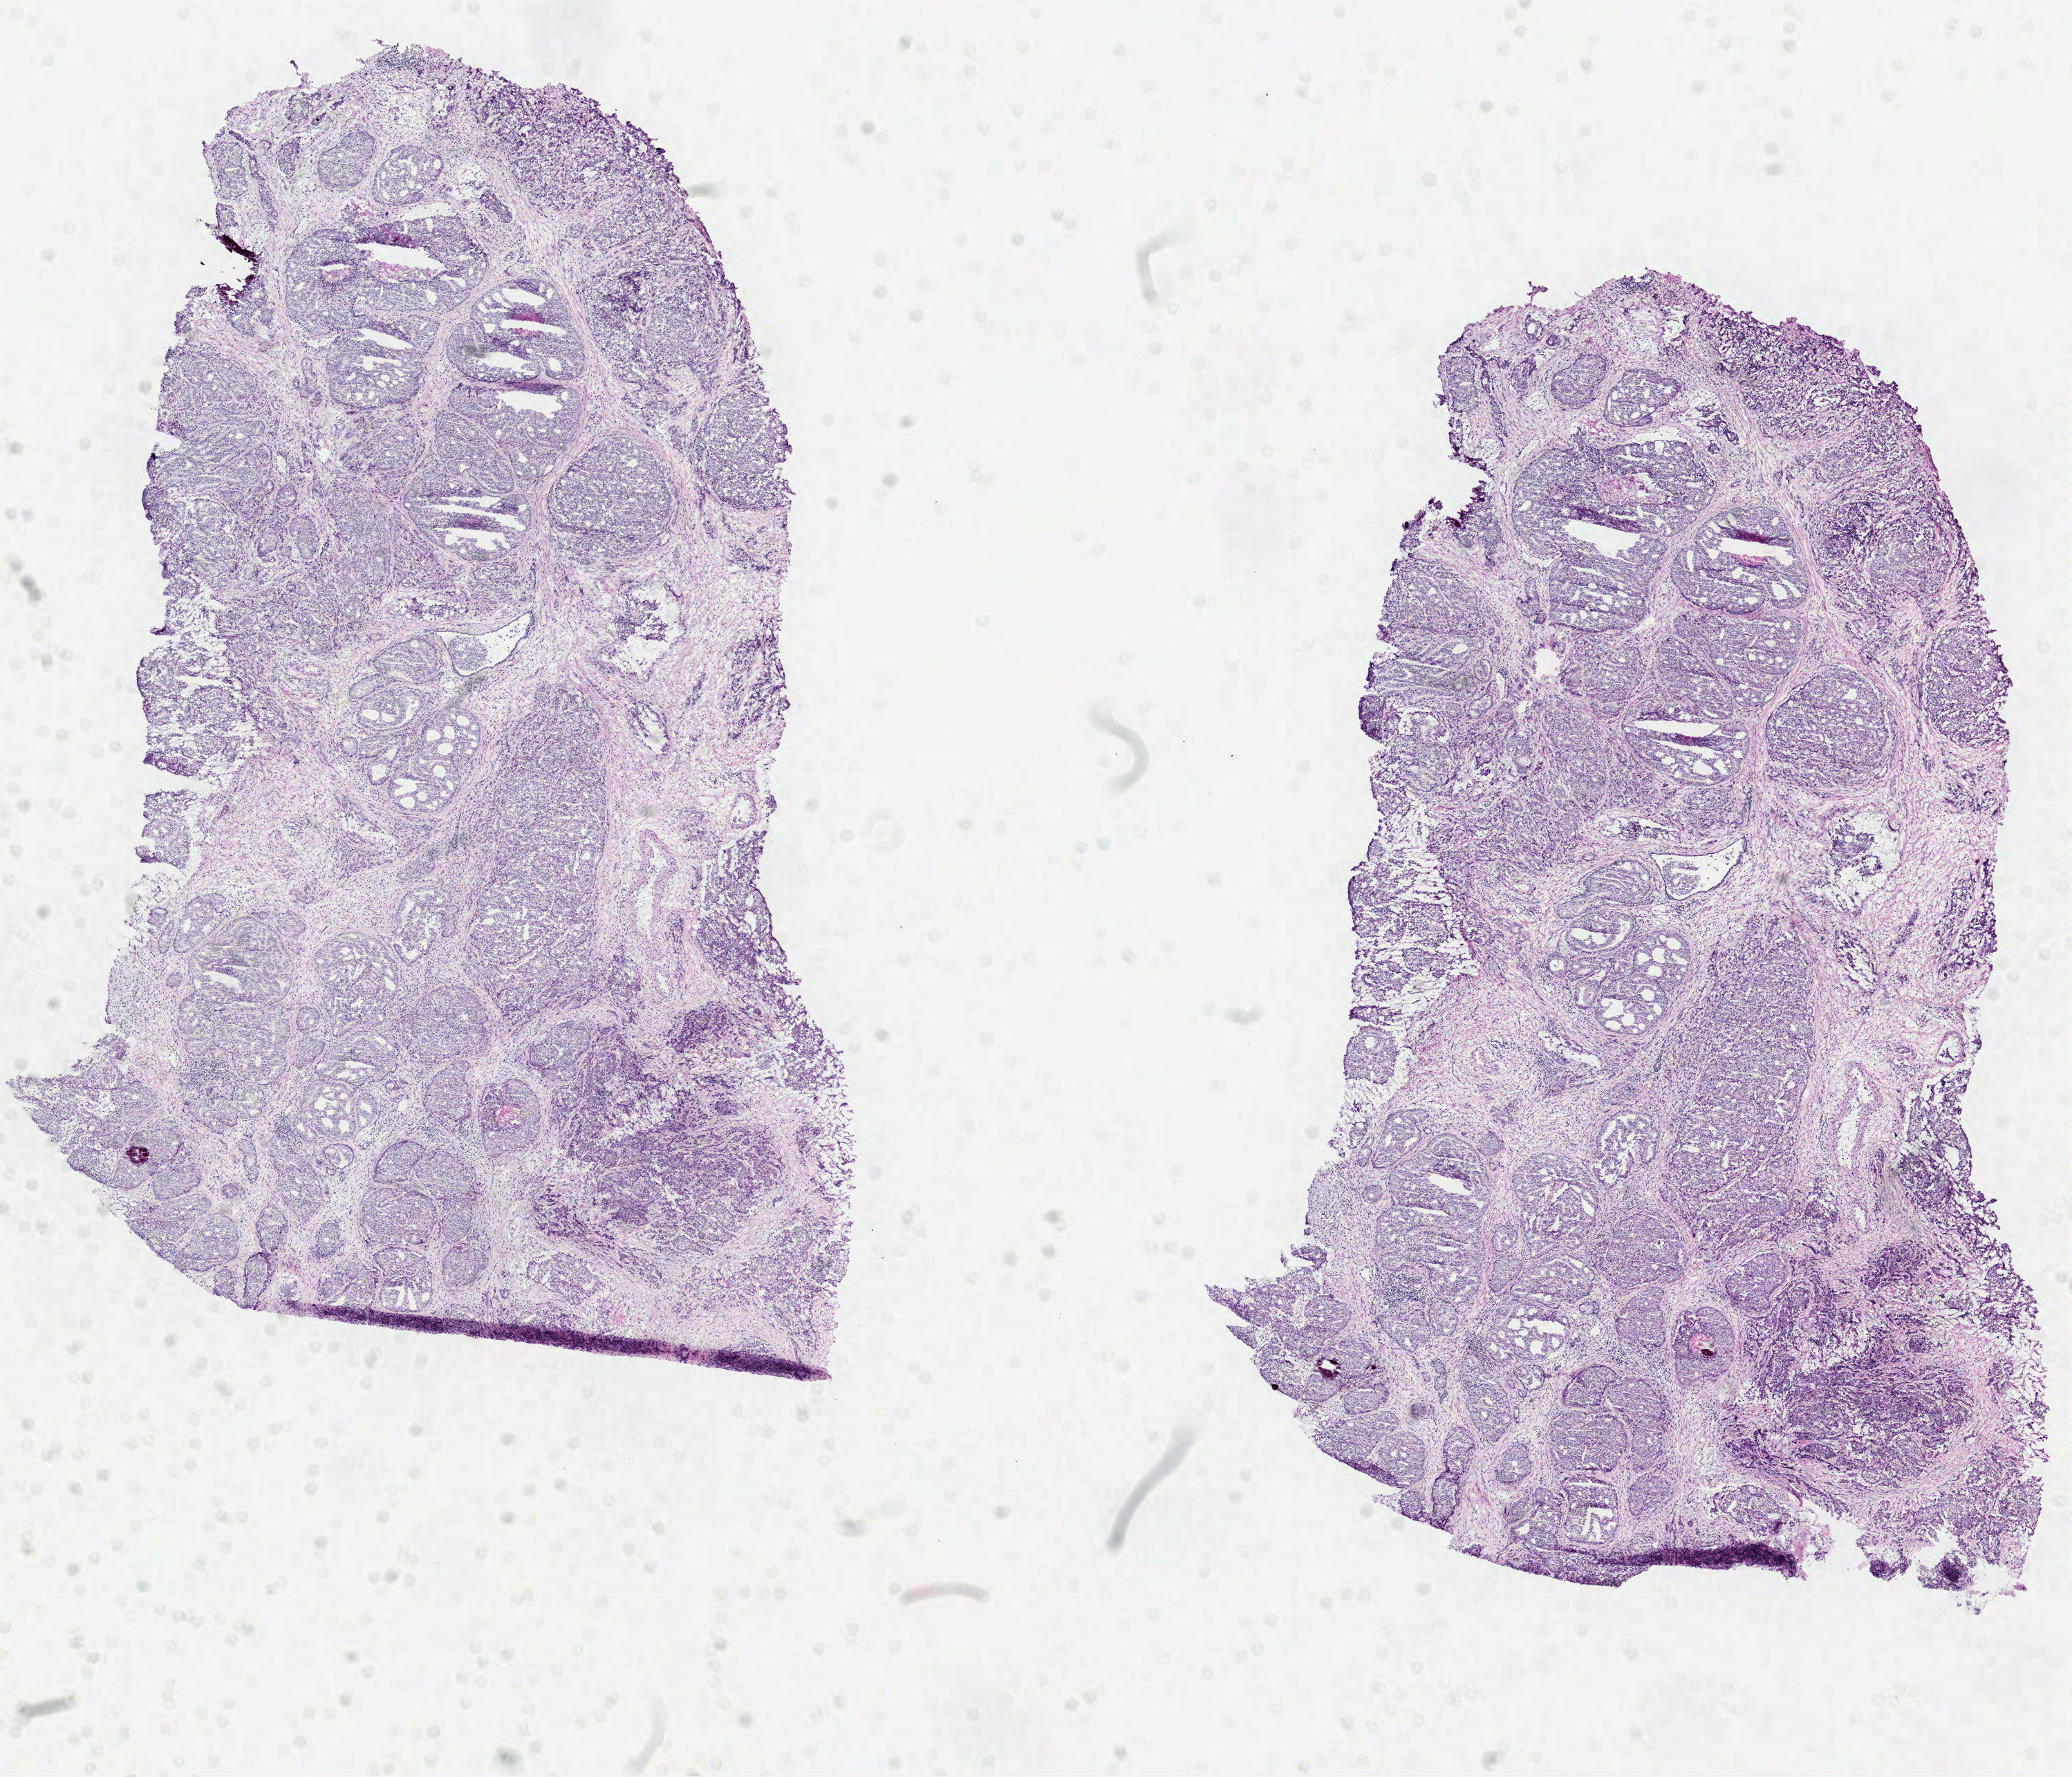
H&E-stained whole-slide image, whole scanned area (about 12.1 x 10.4 mm, acquisition: 40x scan) shown as a low-resolution overview; formalin-fixed paraffin-embedded (FFPE) diagnostic section; sample: primary tumour, prostate. Male patient; age at initial diagnosis 55 years. Gleason score: 7 (3+4).
• lymph nodes positive (case pathology): 0 of 7 examined
• diagnosis: Acinar cell carcinoma (prostate gland)